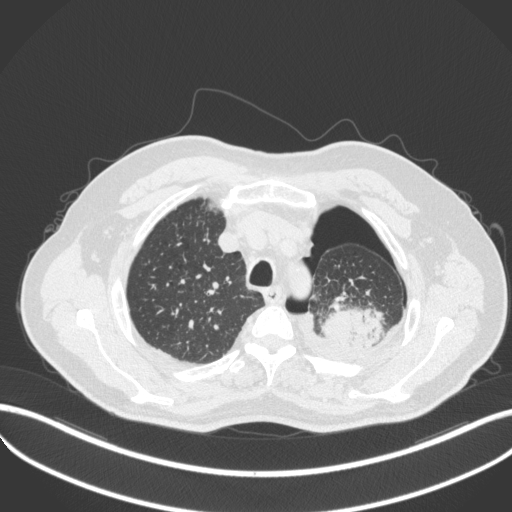
Chest CT, one axial slice; slice 409 of 466 in the series (ordered by position); 120 kVp; lung window (W 1500 / L -600 HU); 512 × 512 image matrix, field of view 400 × 400 mm. Male patient, age 76 years. Case-level facts recorded for this patient, not image findings: clinical TNM (as recorded): T3 N0 M1b.
Outlined on this slice (bounding box drawn by a radiologist):
- lung tumour (recorded histology: adenocarcinoma): bounding box <322,303,387,347> (left, top, right, bottom; pixels)